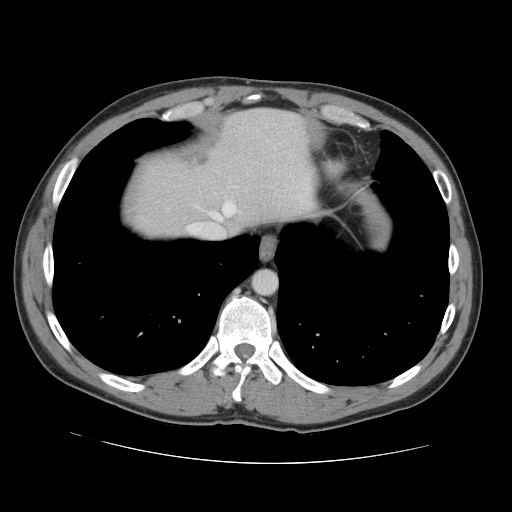
Contrast-enhanced abdominal CT, one axial slice; position 124 of 131 along the scan axis; 120 kVp; intravenous contrast given; soft-tissue window (W 400 / L 40 HU); 2.5 mm slice thickness; 512 × 512 image matrix, field of view 380 × 380 mm. Male patient, age 40 years. From the clinical record (not read from this slice): diagnosis: colorectal cancer liver metastases, imaged before liver resection; multiple liver metastases: yes; largest metastasis: 2.9 cm; chemotherapy before resection: yes.
Structures marked on this image (manually delineated by an expert):
- hepatic veins: box from (x=187, y=202) to (x=235, y=235) px
- liver: (x=136, y=109)–(x=311, y=238)
- planned liver remnant (the part of the liver to remain after resection): (x=142, y=109)–(x=312, y=231)